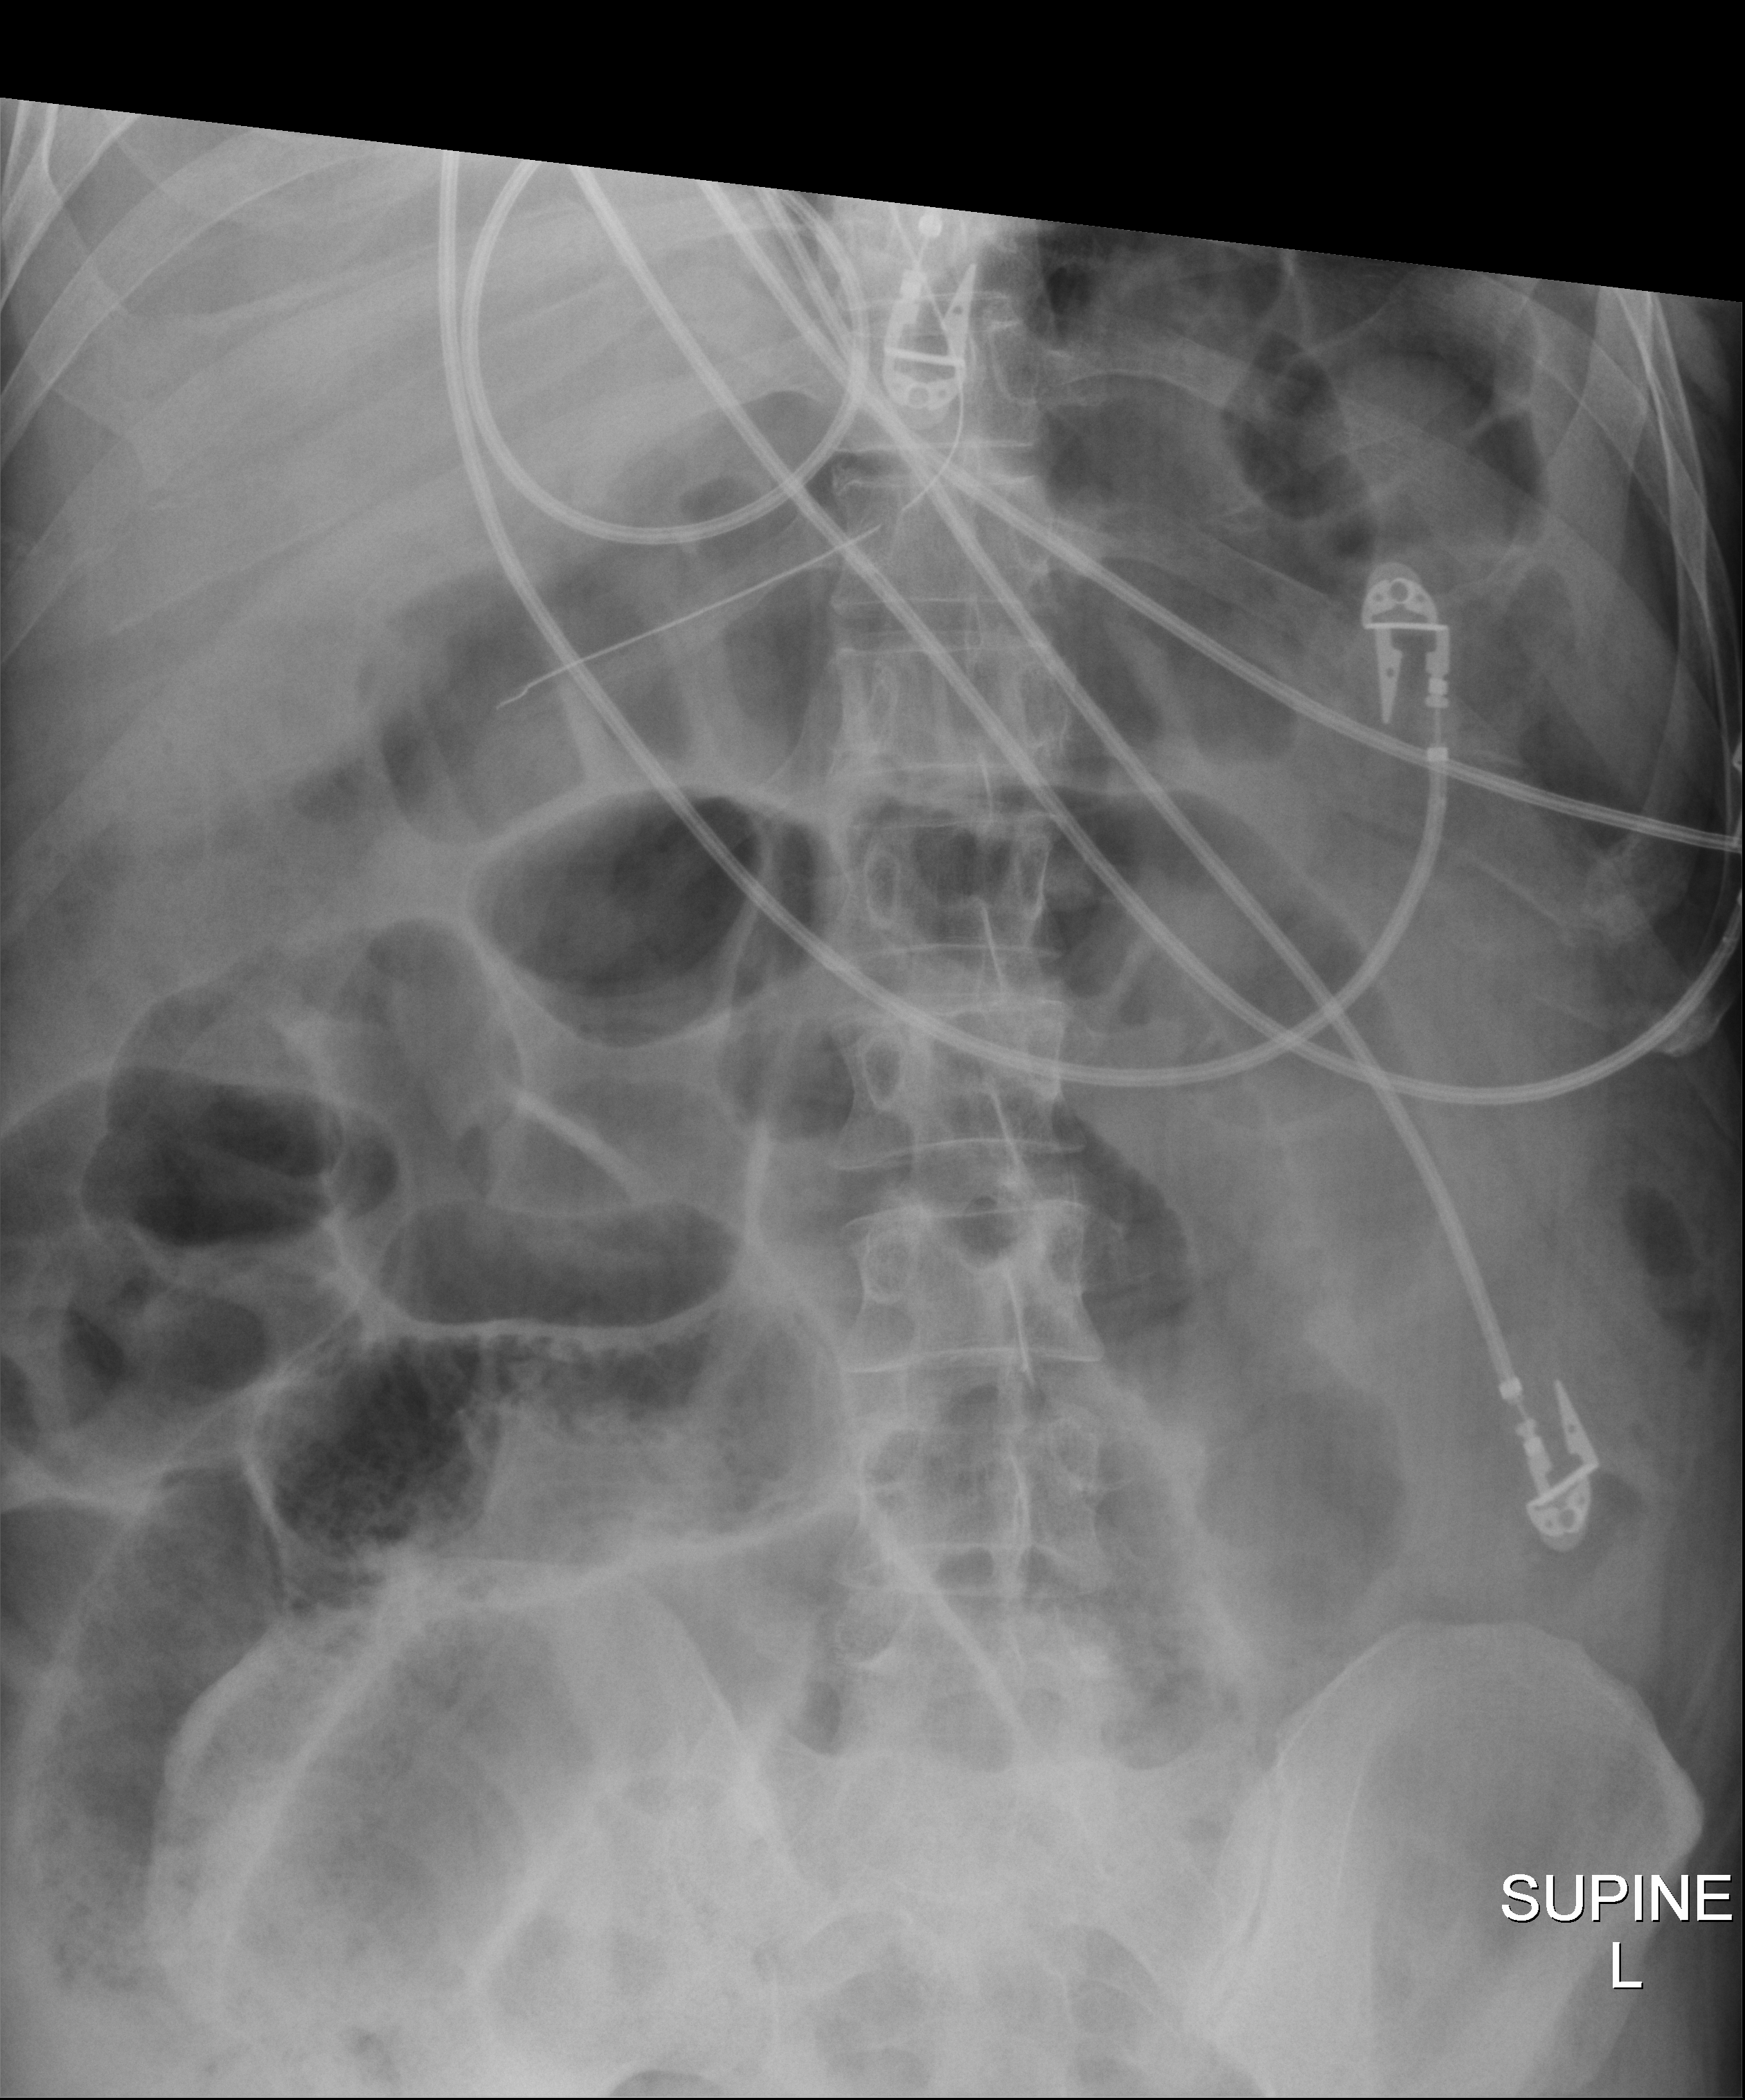
Bedside abdomen radiograph (digital radiography). Patient hospitalised with COVID-19, aged 18–59 years.
Hospital-stay facts (about this admission, not read from this image; timing relative to this image not recorded): length of hospital stay: 50 days.